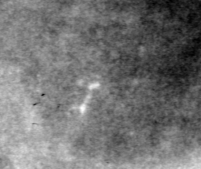
Crop from a digitized film mammogram around one marked abnormality, left breast, CC view, BI-RADS breast density category 4 (scale 1–4).
Calcifications, morphology pleomorphic, distribution clustered; BI-RADS assessment category 4; pathology (as recorded): benign.